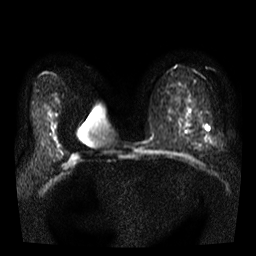
Breast MRI, one axial slice; position 21 of 38 along the scan axis; diffusion-weighted series; image 2 of 4 stored at this slice position (different b-values; order by instance number); 3 T; 5 mm slice thickness; 256 × 256 image matrix, field of view 320 × 320 mm. Female patient.
Annotated regions visible in this slice (outlined manually by an expert reader):
- tumour on diffusion-weighted imaging: bounding box (x1, y1, x2, y2) in pixels: (206, 126, 210, 131)